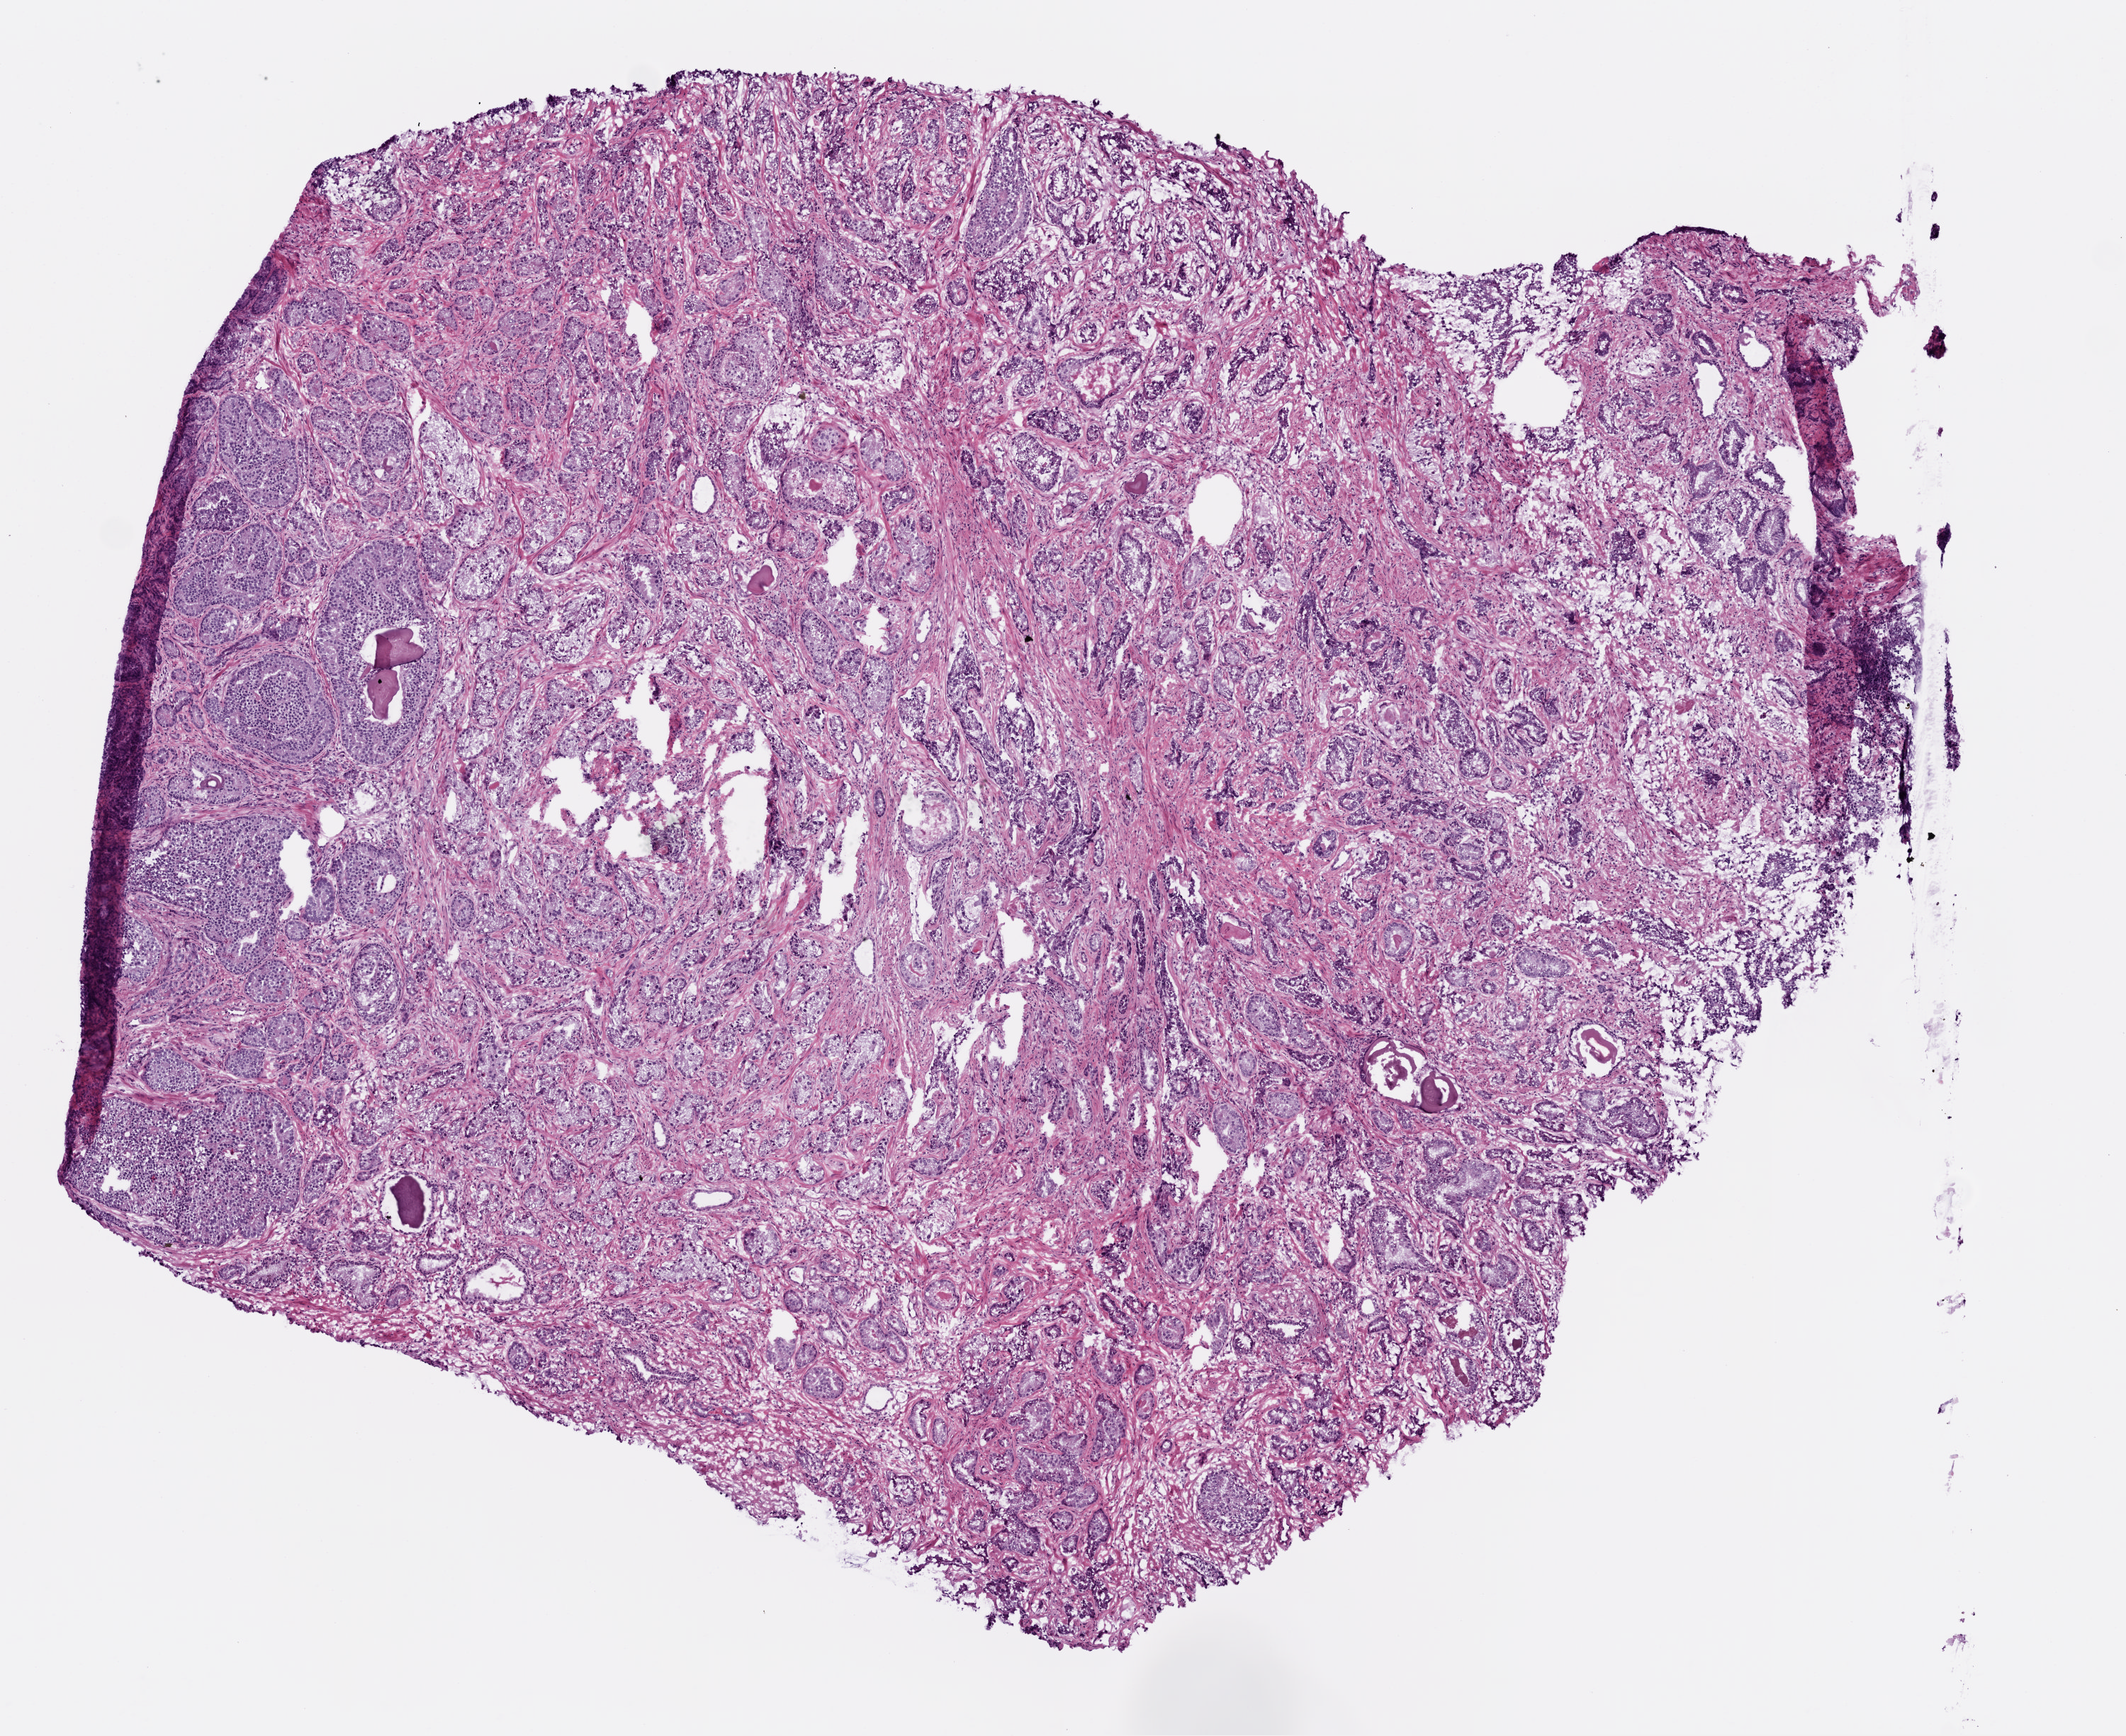
H&E whole-slide image — shown as a low-resolution overview of the whole scanned area (about 6.0 x 4.9 mm); frozen section from the top of the tissue portion; primary tumour sample from the prostate. Male patient; age at initial diagnosis 72 years. Pathologist review of this section (percent, as recorded): tumour cells 60%, tumour nuclei 70%.
Diagnosis: Acinar cell carcinoma (prostate gland).